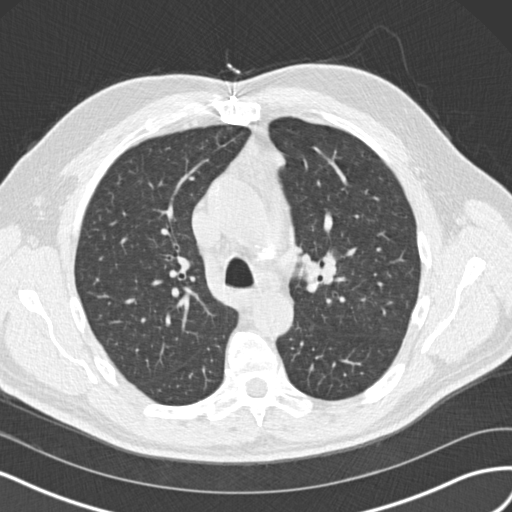
Axial slice from a low-dose chest CT screening exam, first (baseline) screen, lung window (W 1500 / L -600 HU), slice 52 of 160 in the series, 512 × 512 image matrix, field of view 360 × 360 mm. Male, age 65 years at enrolment. Former smoker at enrolment.
Expert-annotated lung lesion, bounding box <302,243,354,297> (left, top, right, bottom; pixels). The screening reader recorded 4 non-calcified nodules or masses ≥4 mm on this exam (left upper lobe, left upper lobe, right upper lobe, right middle lobe); which of them this box marks is not recorded. Official screen result: positive, change unspecified: nodule(s) >= 4 mm or enlarging nodule(s), mass(es), or other non-specific abnormalities suspicious for lung cancer. Later outcome: lung cancer diagnosed 945 days after this screen — acinar cell carcinoma, left upper lobe, stage IA (AJCC 6th edition), 25 mm at pathology.